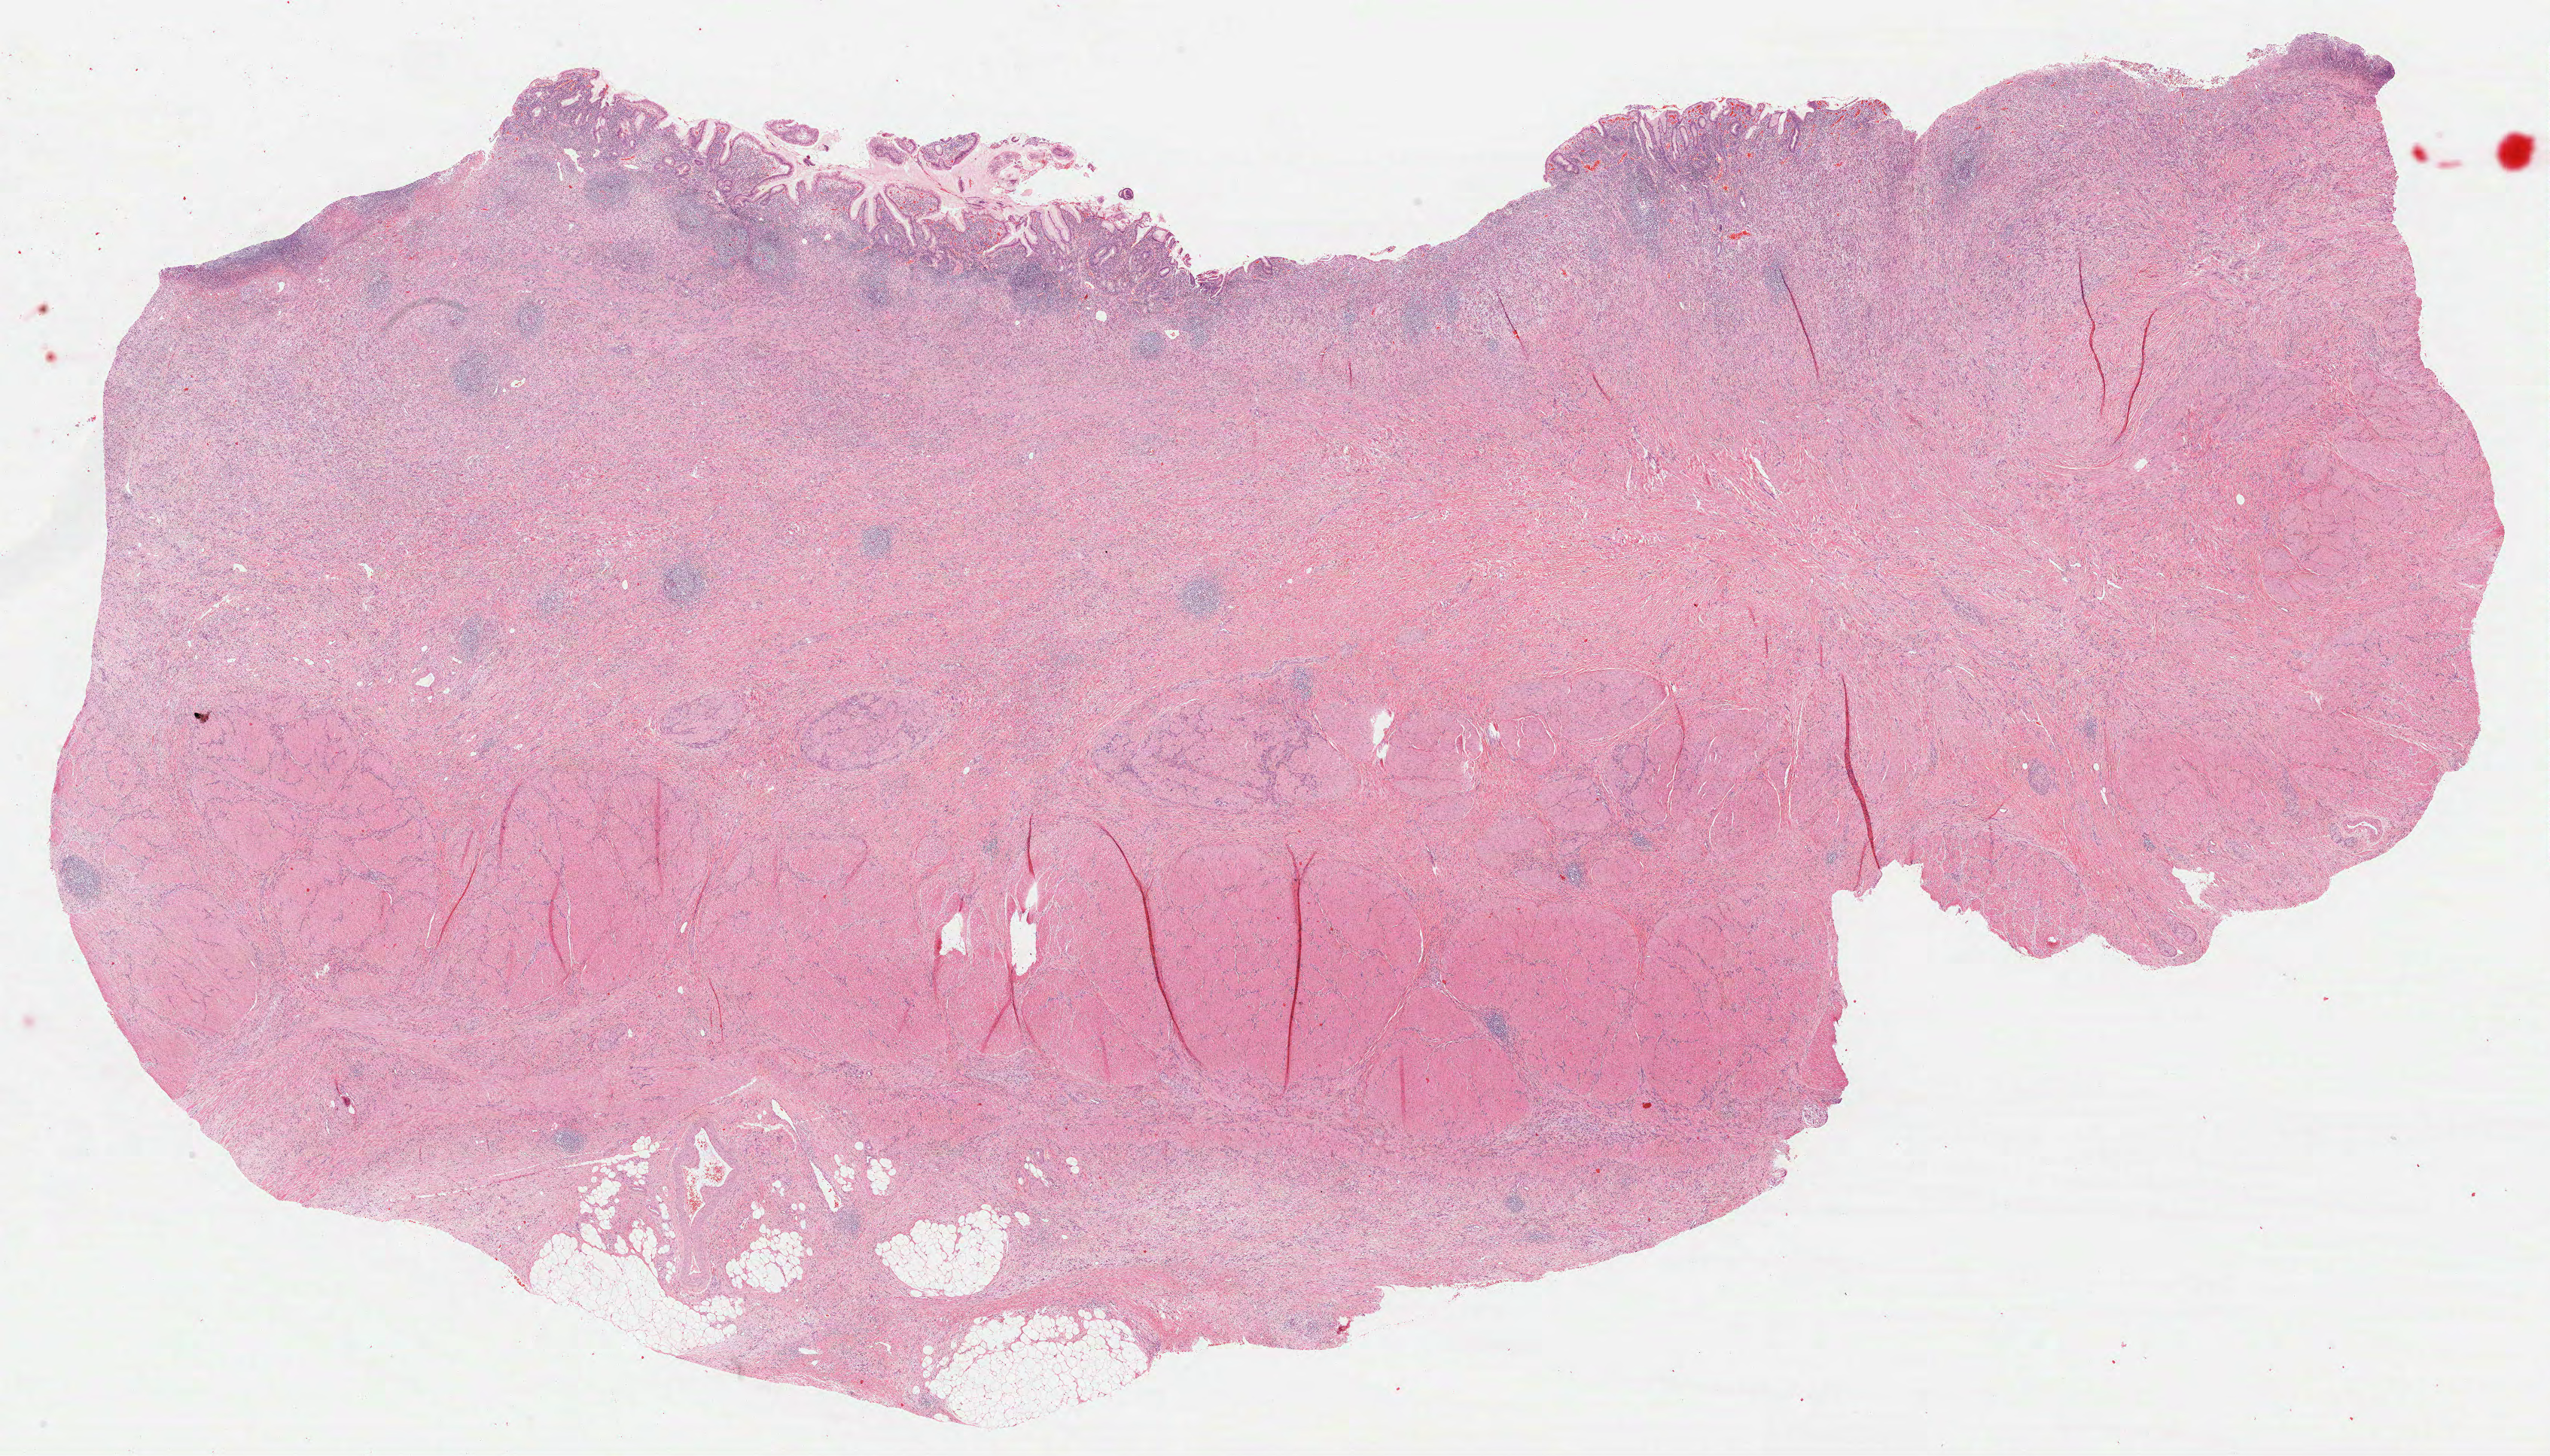
Whole-slide histology image, H&E — low-resolution overview of the scanned area, about 27.3 x 15.6 mm; formalin-fixed paraffin-embedded (FFPE) diagnostic section; primary tumour sample from the stomach. Female, age 63 years at initial diagnosis. Histologic grade: G3 (poorly differentiated).
AJCC pathologic stage: IIIB (7th edition). TNM: T4b N1 M0. Diagnosis: Carcinoma, diffuse type (fundus of stomach).